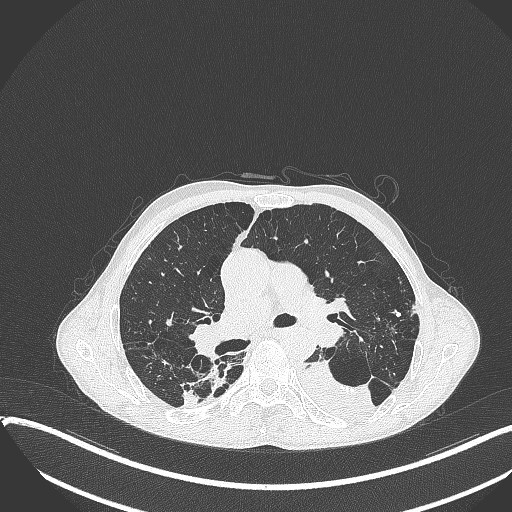
Chest CT, one axial slice. Position 232 of 401 along the scan axis. Reconstruction kernel B70f. Lung window (W 1500 / L -600 HU). 1 mm slice thickness. 512 × 512 image matrix, field of view 400 × 400 mm. Male patient, age 57 years. From the clinical record (not read from this slice): clinical TNM (as recorded): T4 N0 M0.
Outlined on this slice (rectangle marked by the reading radiologist):
- lung tumour (recorded histology: squamous cell carcinoma): bounding box [x1, y1, x2, y2] px = [298, 355, 377, 421]